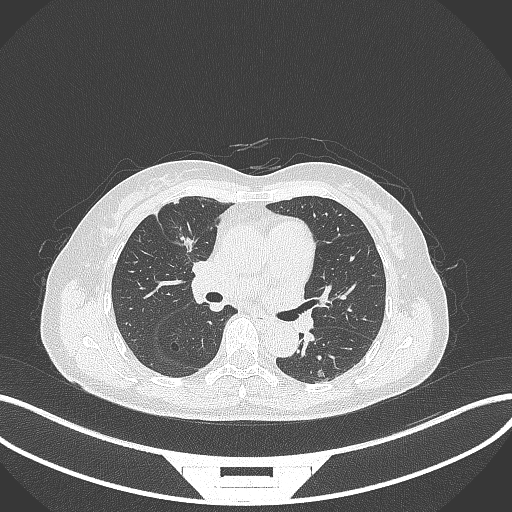
Chest CT, one axial slice; slice 168 of 284 in the series (ordered by position); reconstruction kernel B70f; 120 kVp; lung window (W 1500 / L -600 HU); 1 mm slice thickness; 512 × 512 image matrix. Female patient, age 51 years. Case-level facts recorded for this patient, not image findings: clinical TNM (as recorded): T1c N0 M0; histopathological grade: G2.
Annotated regions visible in this slice (rectangle marked by the reading radiologist):
- lung tumour (recorded histology: adenocarcinoma): bounding box [x1, y1, x2, y2] px = [176, 229, 195, 255]